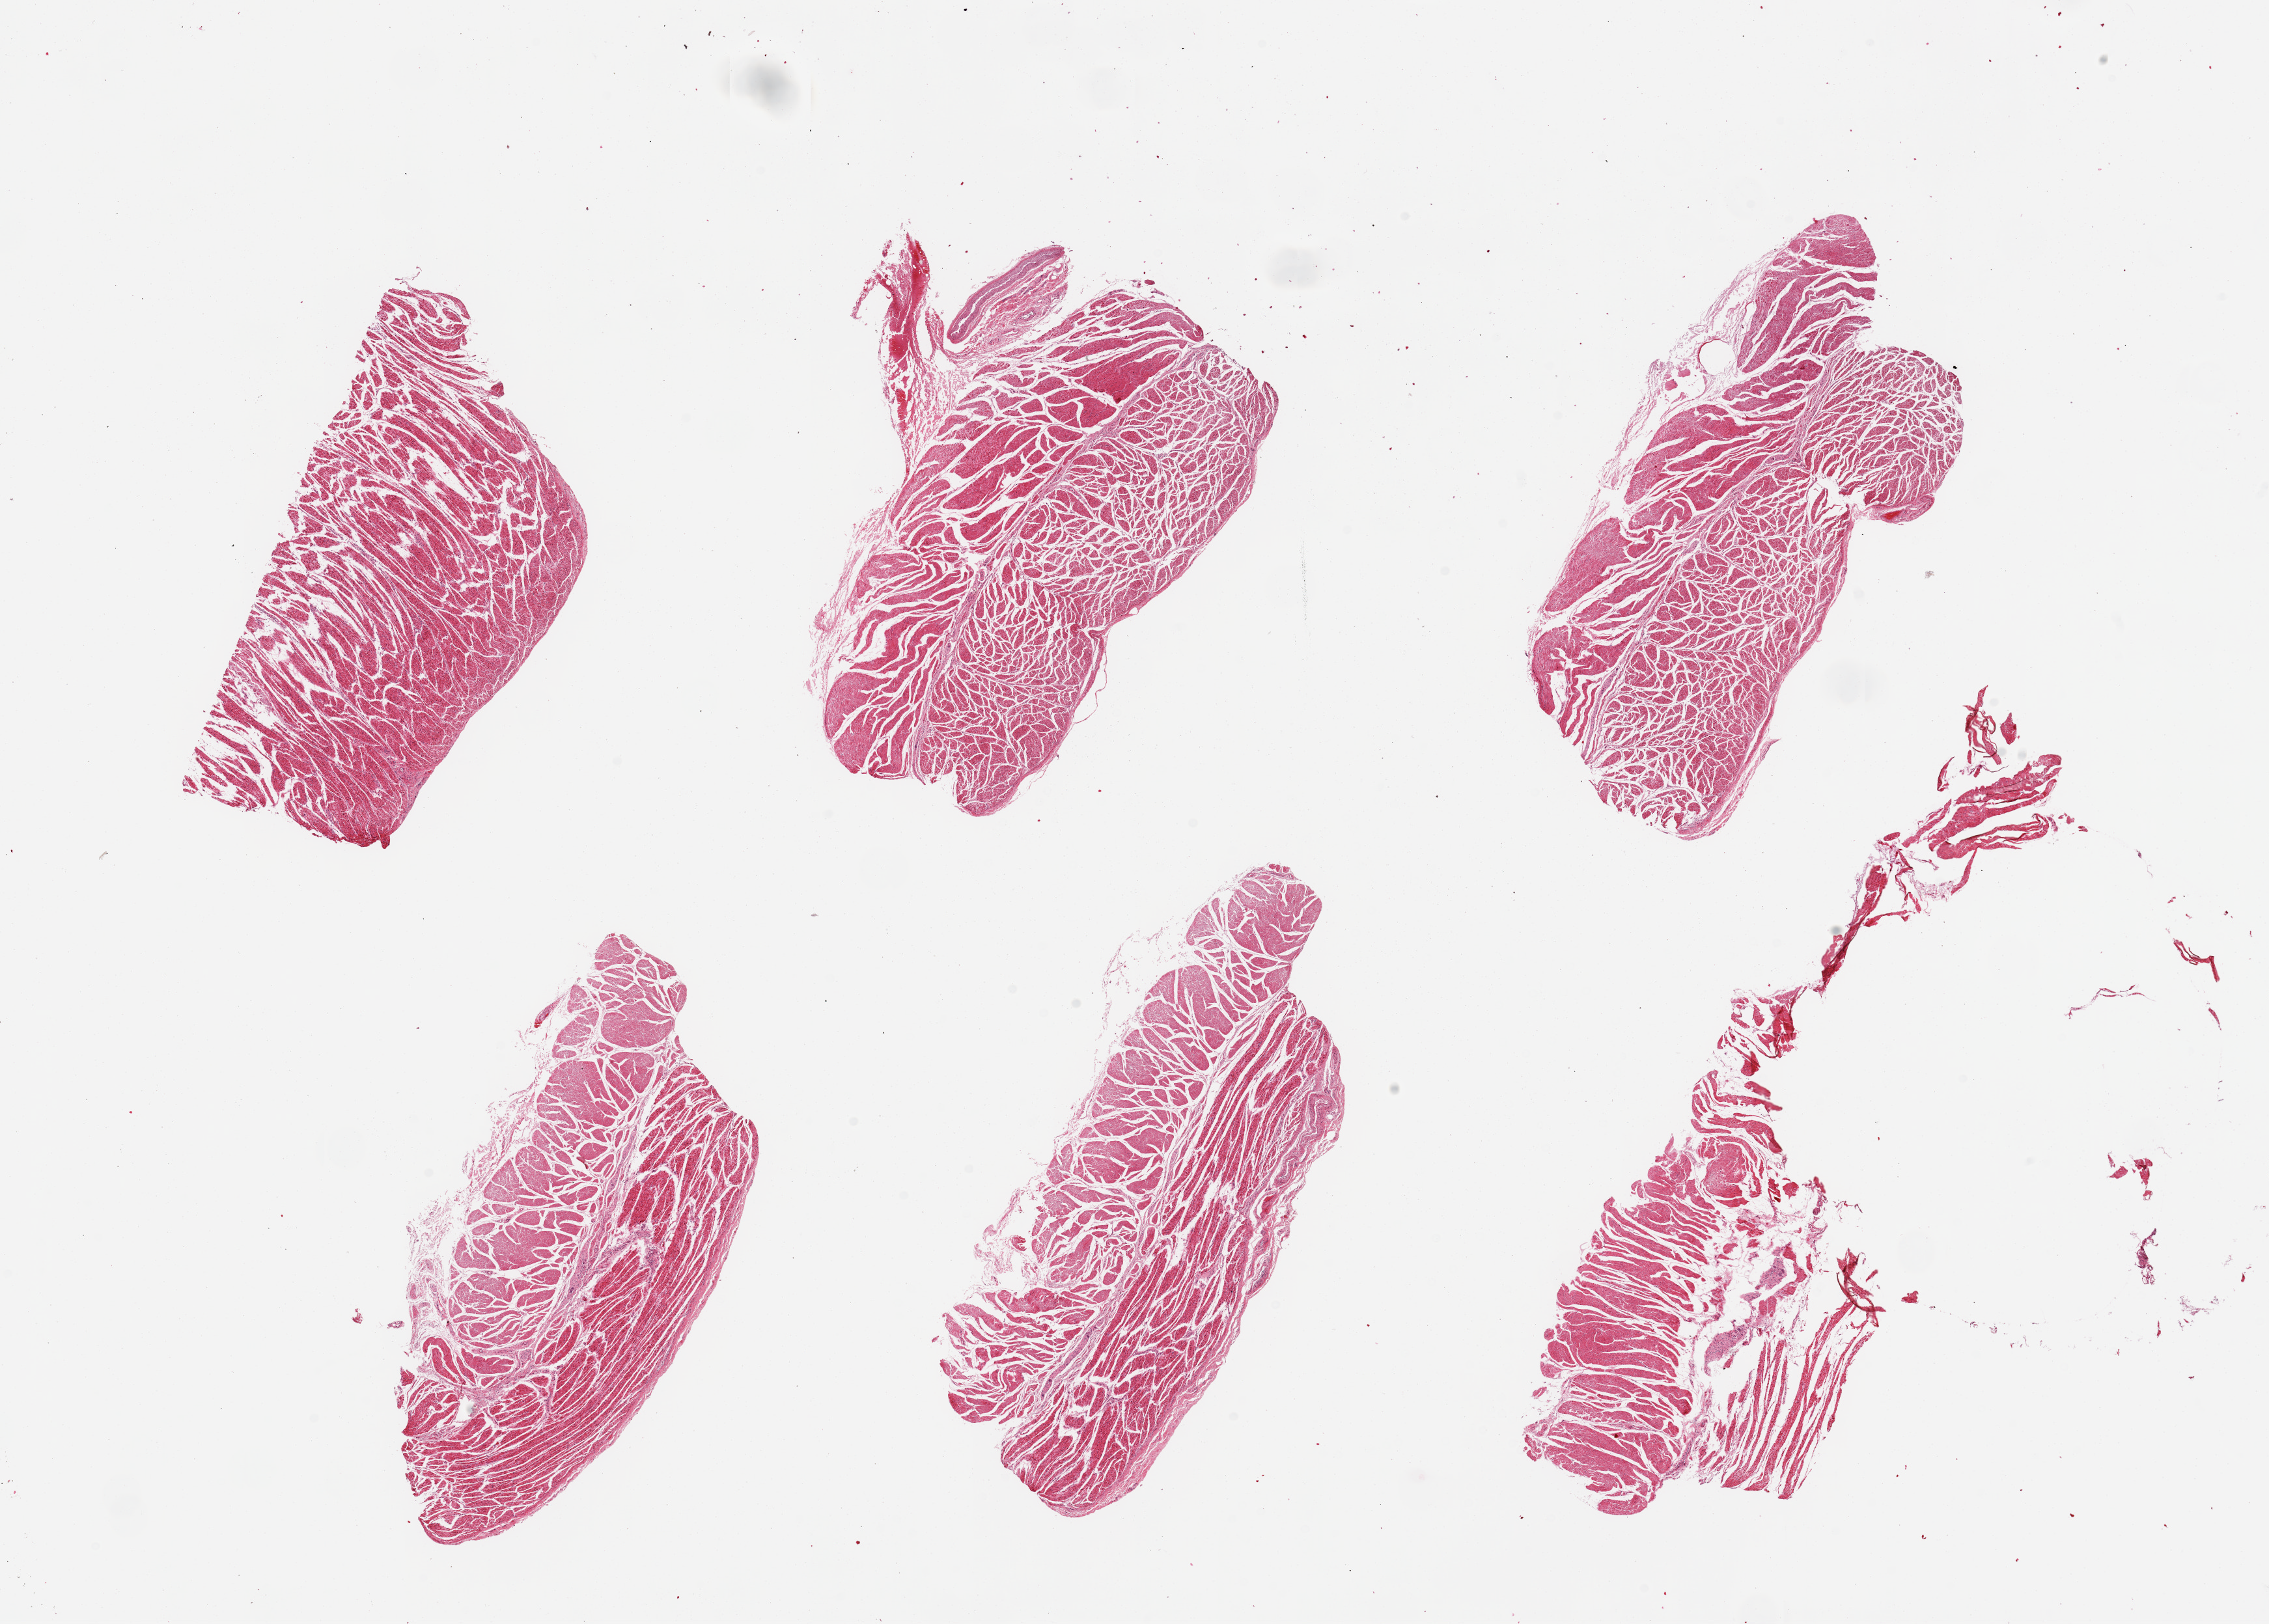
Hematoxylin and eosin (H&E) whole-slide image, whole scanned area (about 27.6 x 19.7 mm, slide scanned at 20x) shown as a low-resolution overview, PAXgene-fixed paraffin-embedded (PFPE) section, target tissue: esophageal muscle, tissue donor sample. Male donor.
Pathologist's review note for this sample: 6 pieces, all muscularis, good specimens.